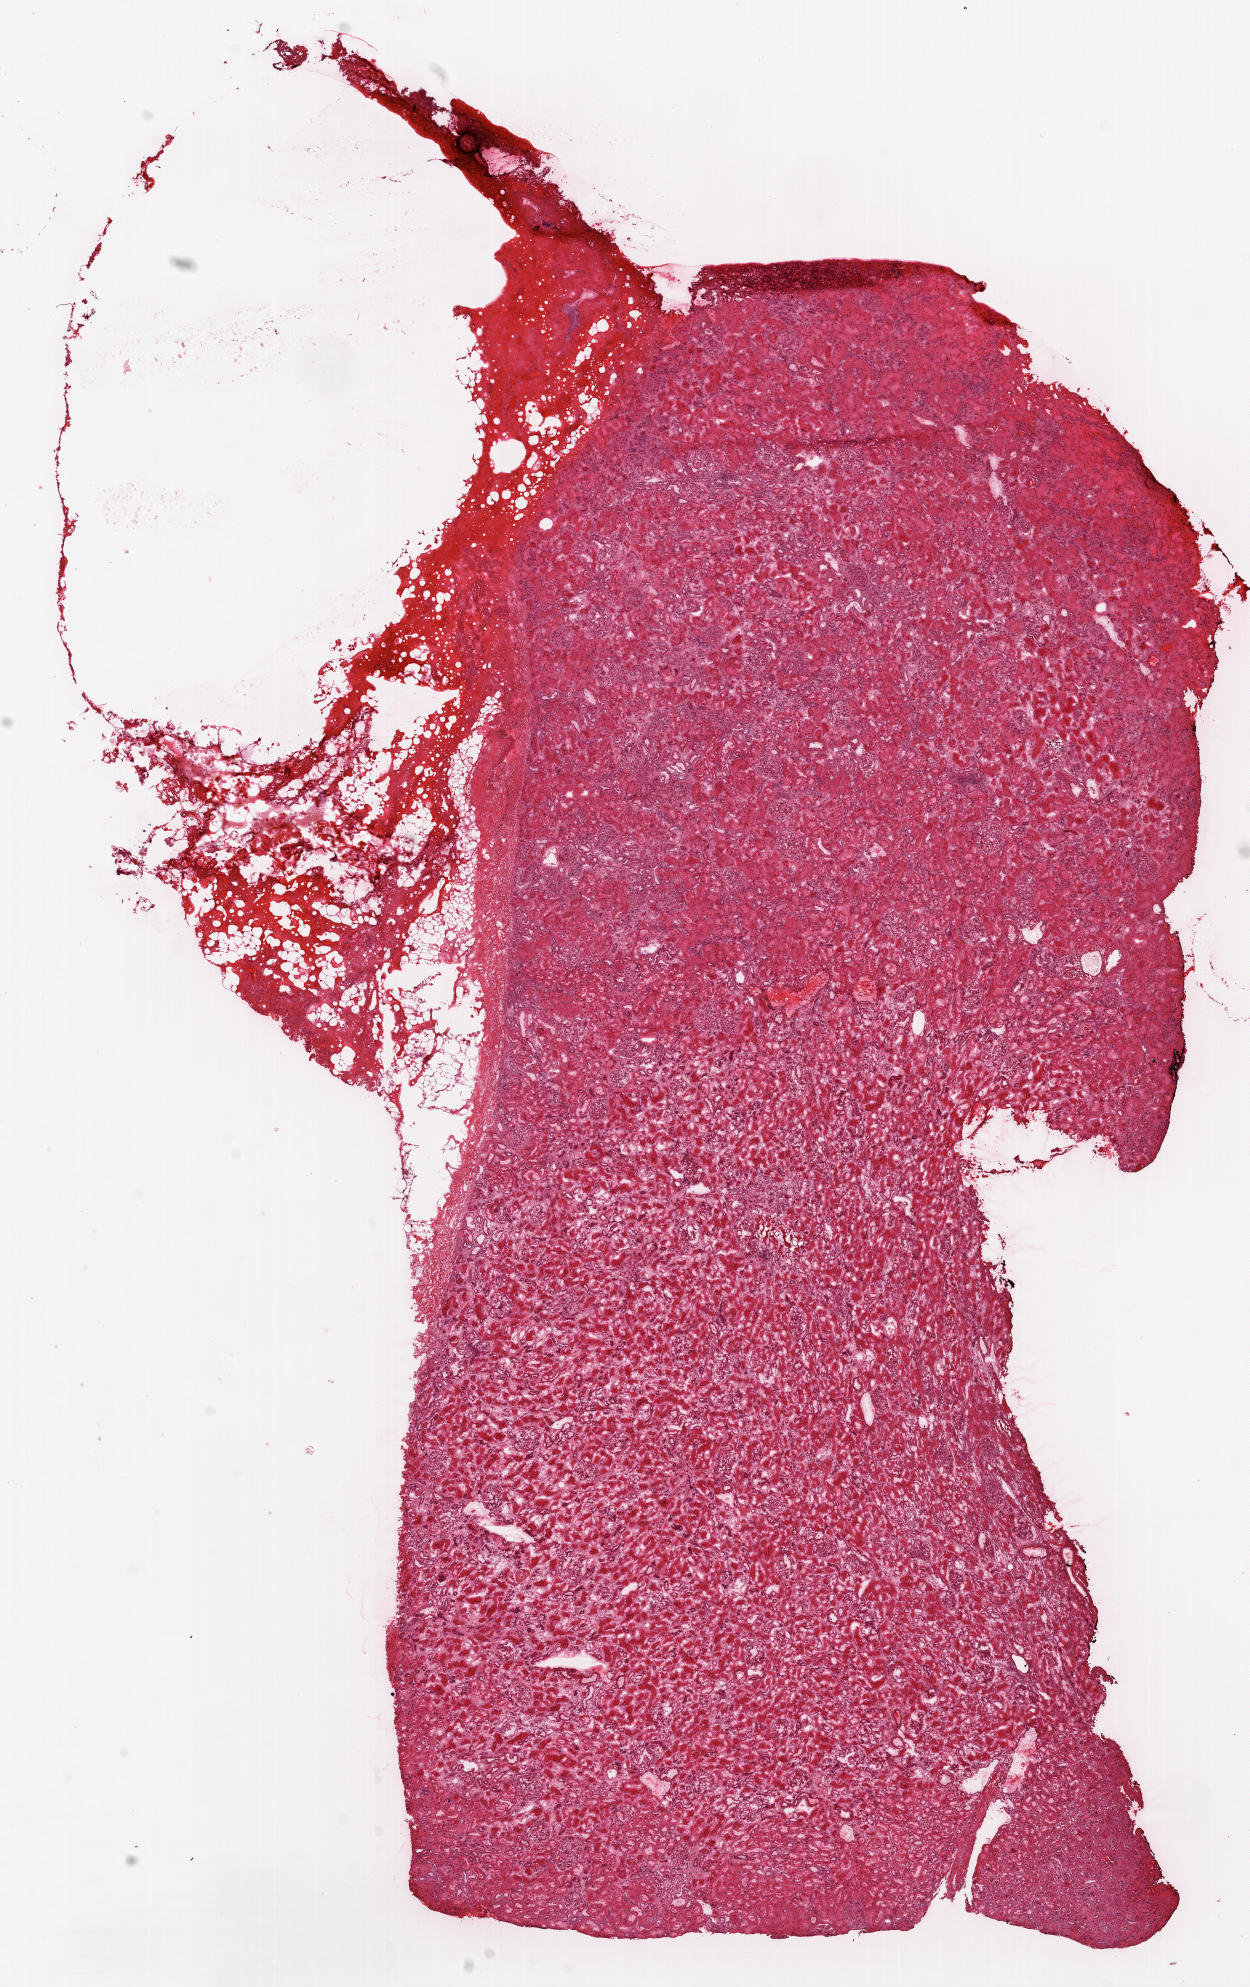
Digitized H&E-stained tissue section (whole slide) — a low-resolution overview of the entire scanned area, about 10.0 x 15.9 mm (from a 20x scan); frozen section from the top of the tissue portion; sample: solid tissue normal (non-tumour tissue), kidney. Patient: male, age at initial diagnosis 61 years.
This section: solid tissue normal (non-tumour) sample from the same patient. Patient diagnosis: Clear cell adenocarcinoma, NOS.